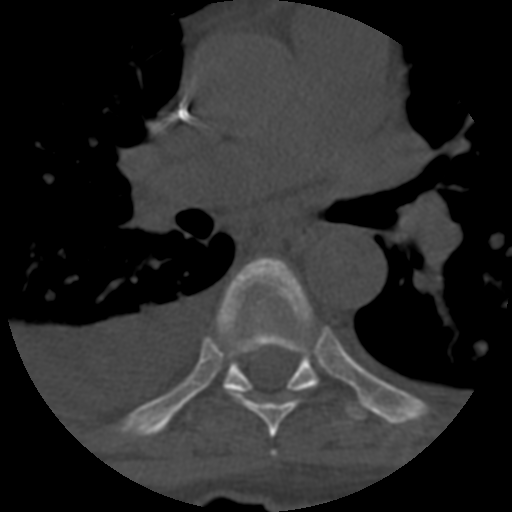
CT including the spine, one axial slice; position 427 of 708 along the scan axis; reconstruction kernel STANDARD; 120 kVp; one of 3 acquisitions stored at this slice position; bone window (W 1800 / L 400 HU); 512 × 512 image matrix, field of view 160 × 160 mm. Patient age 55 years. From the clinical record (not read from this slice): primary cancer: colon.
Annotated regions visible in this slice (semi-automatic segmentation, software-assisted and operator-edited):
- T6 vertebra: bounding box <218,264,310,438> (left, top, right, bottom; pixels)
- T7 vertebra: <222,259,365,421>